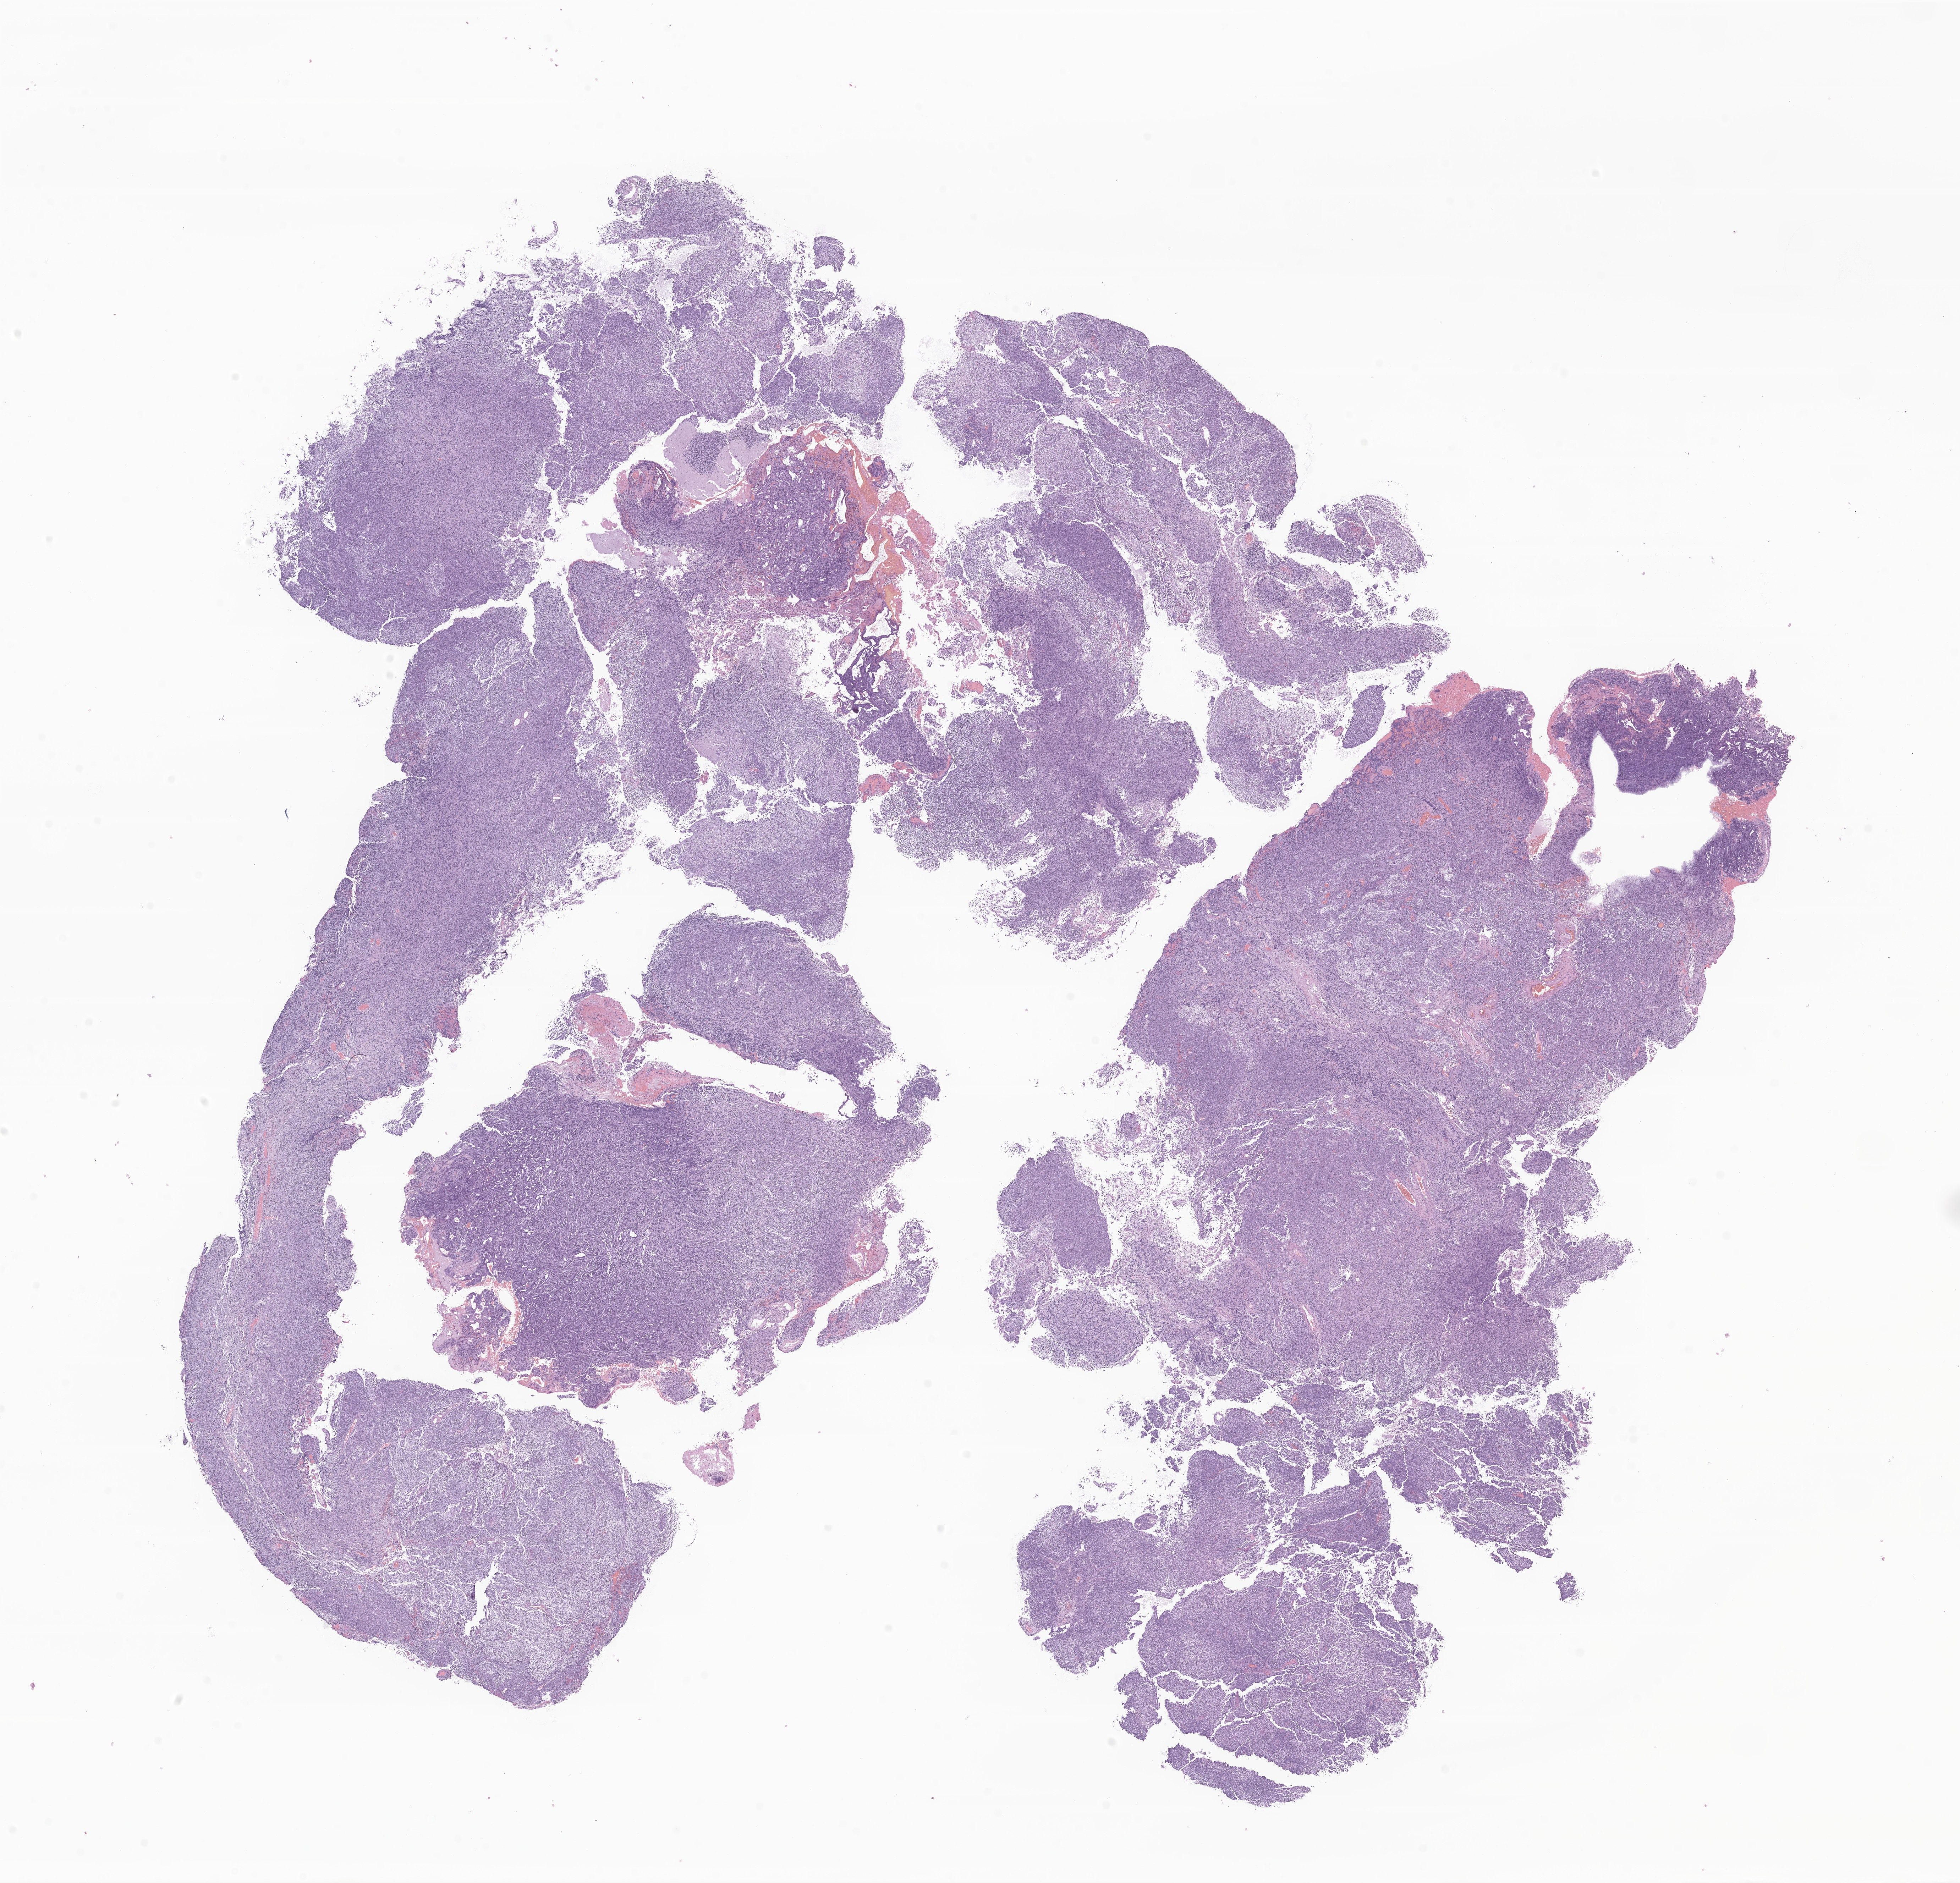
Haematoxylin and eosin whole-slide image of tumor tissue from the brain, low-resolution overview of the scanned area, about 23.3 x 22.4 mm, formalin-fixed, paraffin-embedded (FFPE) tissue. Patient male; age 149 months (12 years 5 months).
Diagnosis (ICD-O-3 morphology term): Medulloblastoma, NOS.